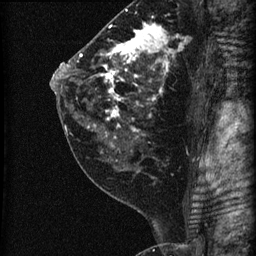
Breast MRI (dynamic contrast-enhanced), one sagittal slice; position 37 of 60 along the scan axis; dynamic contrast-enhanced series, image 2 of 3 at this slice position (ordered by acquisition); 1.5 T; TE 4.2 ms, TR 22.7 ms; 1.8 mm slice thickness; 256 × 256 image matrix. Patient: female, 45 years. From the clinical record (not read from this slice): setting: breast cancer imaged before/during neoadjuvant chemotherapy; receptor status: HR-positive, HER2-negative.
Outlined on this slice (semi-automatically segmented with operator editing):
- analysis volume of interest (the breast-tissue region the enhancement analysis was run in; not a lesion): bounding box (x1, y1, x2, y2) in pixels: (74, 11, 205, 140)
- tumour enhancement mask (voxels above the 90 % enhancement threshold inside the analysis volume of interest): (79, 23, 182, 138)